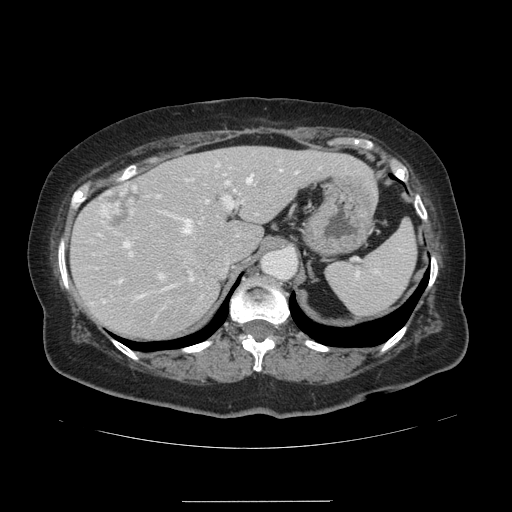
Contrast-enhanced abdominal CT, one axial slice. Slice 92 of 141 in the series (ordered by position). 120 kVp. Intravenous contrast given. Soft-tissue window (W 400 / L 40 HU). 2.5 mm slice thickness. 512 × 512 image matrix, field of view 393 × 393 mm. Female patient, age 74 years. Case-level facts recorded for this patient, not image findings: diagnosis: colorectal cancer liver metastases, imaged before liver resection; multiple liver metastases: yes; largest metastasis: 7 cm; disease in both lobes: yes.
Structures marked on this image (outlined manually by an expert reader):
- hepatic veins: bounding box (x1, y1, x2, y2) in pixels: (134, 170, 281, 298)
- liver: (72, 147, 365, 340)
- planned liver remnant (the part of the liver to remain after resection): (72, 147, 365, 340)
- portal vein (with intrahepatic branches): (119, 164, 298, 282)
- liver metastasis: (100, 182, 140, 232)